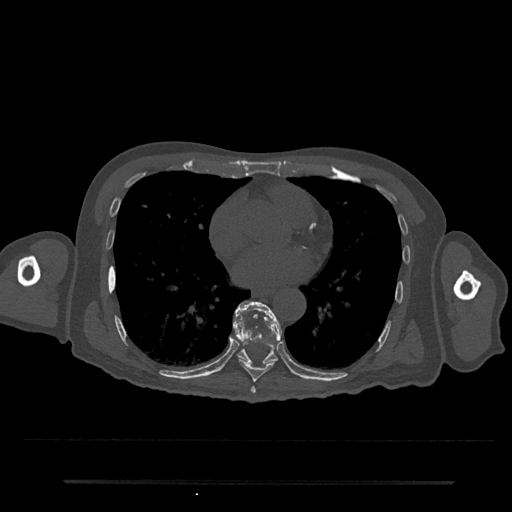
CT including the spine, one axial slice; position 400 of 797 along the scan axis; reconstruction kernel Br40s/3; bone window (W 1800 / L 400 HU); 0.5 mm slice thickness; 512 × 512 image matrix. Patient: male, 74 years. Case-level facts recorded for this patient, not image findings: primary cancer: prostate.
Annotated regions visible in this slice (semi-automatic segmentation, software-assisted and operator-edited):
- T7 vertebra: box from (x=250, y=386) to (x=256, y=394) px
- T8 vertebra: (x=233, y=301)–(x=280, y=382)
- T9 vertebra: (x=233, y=301)–(x=282, y=364)